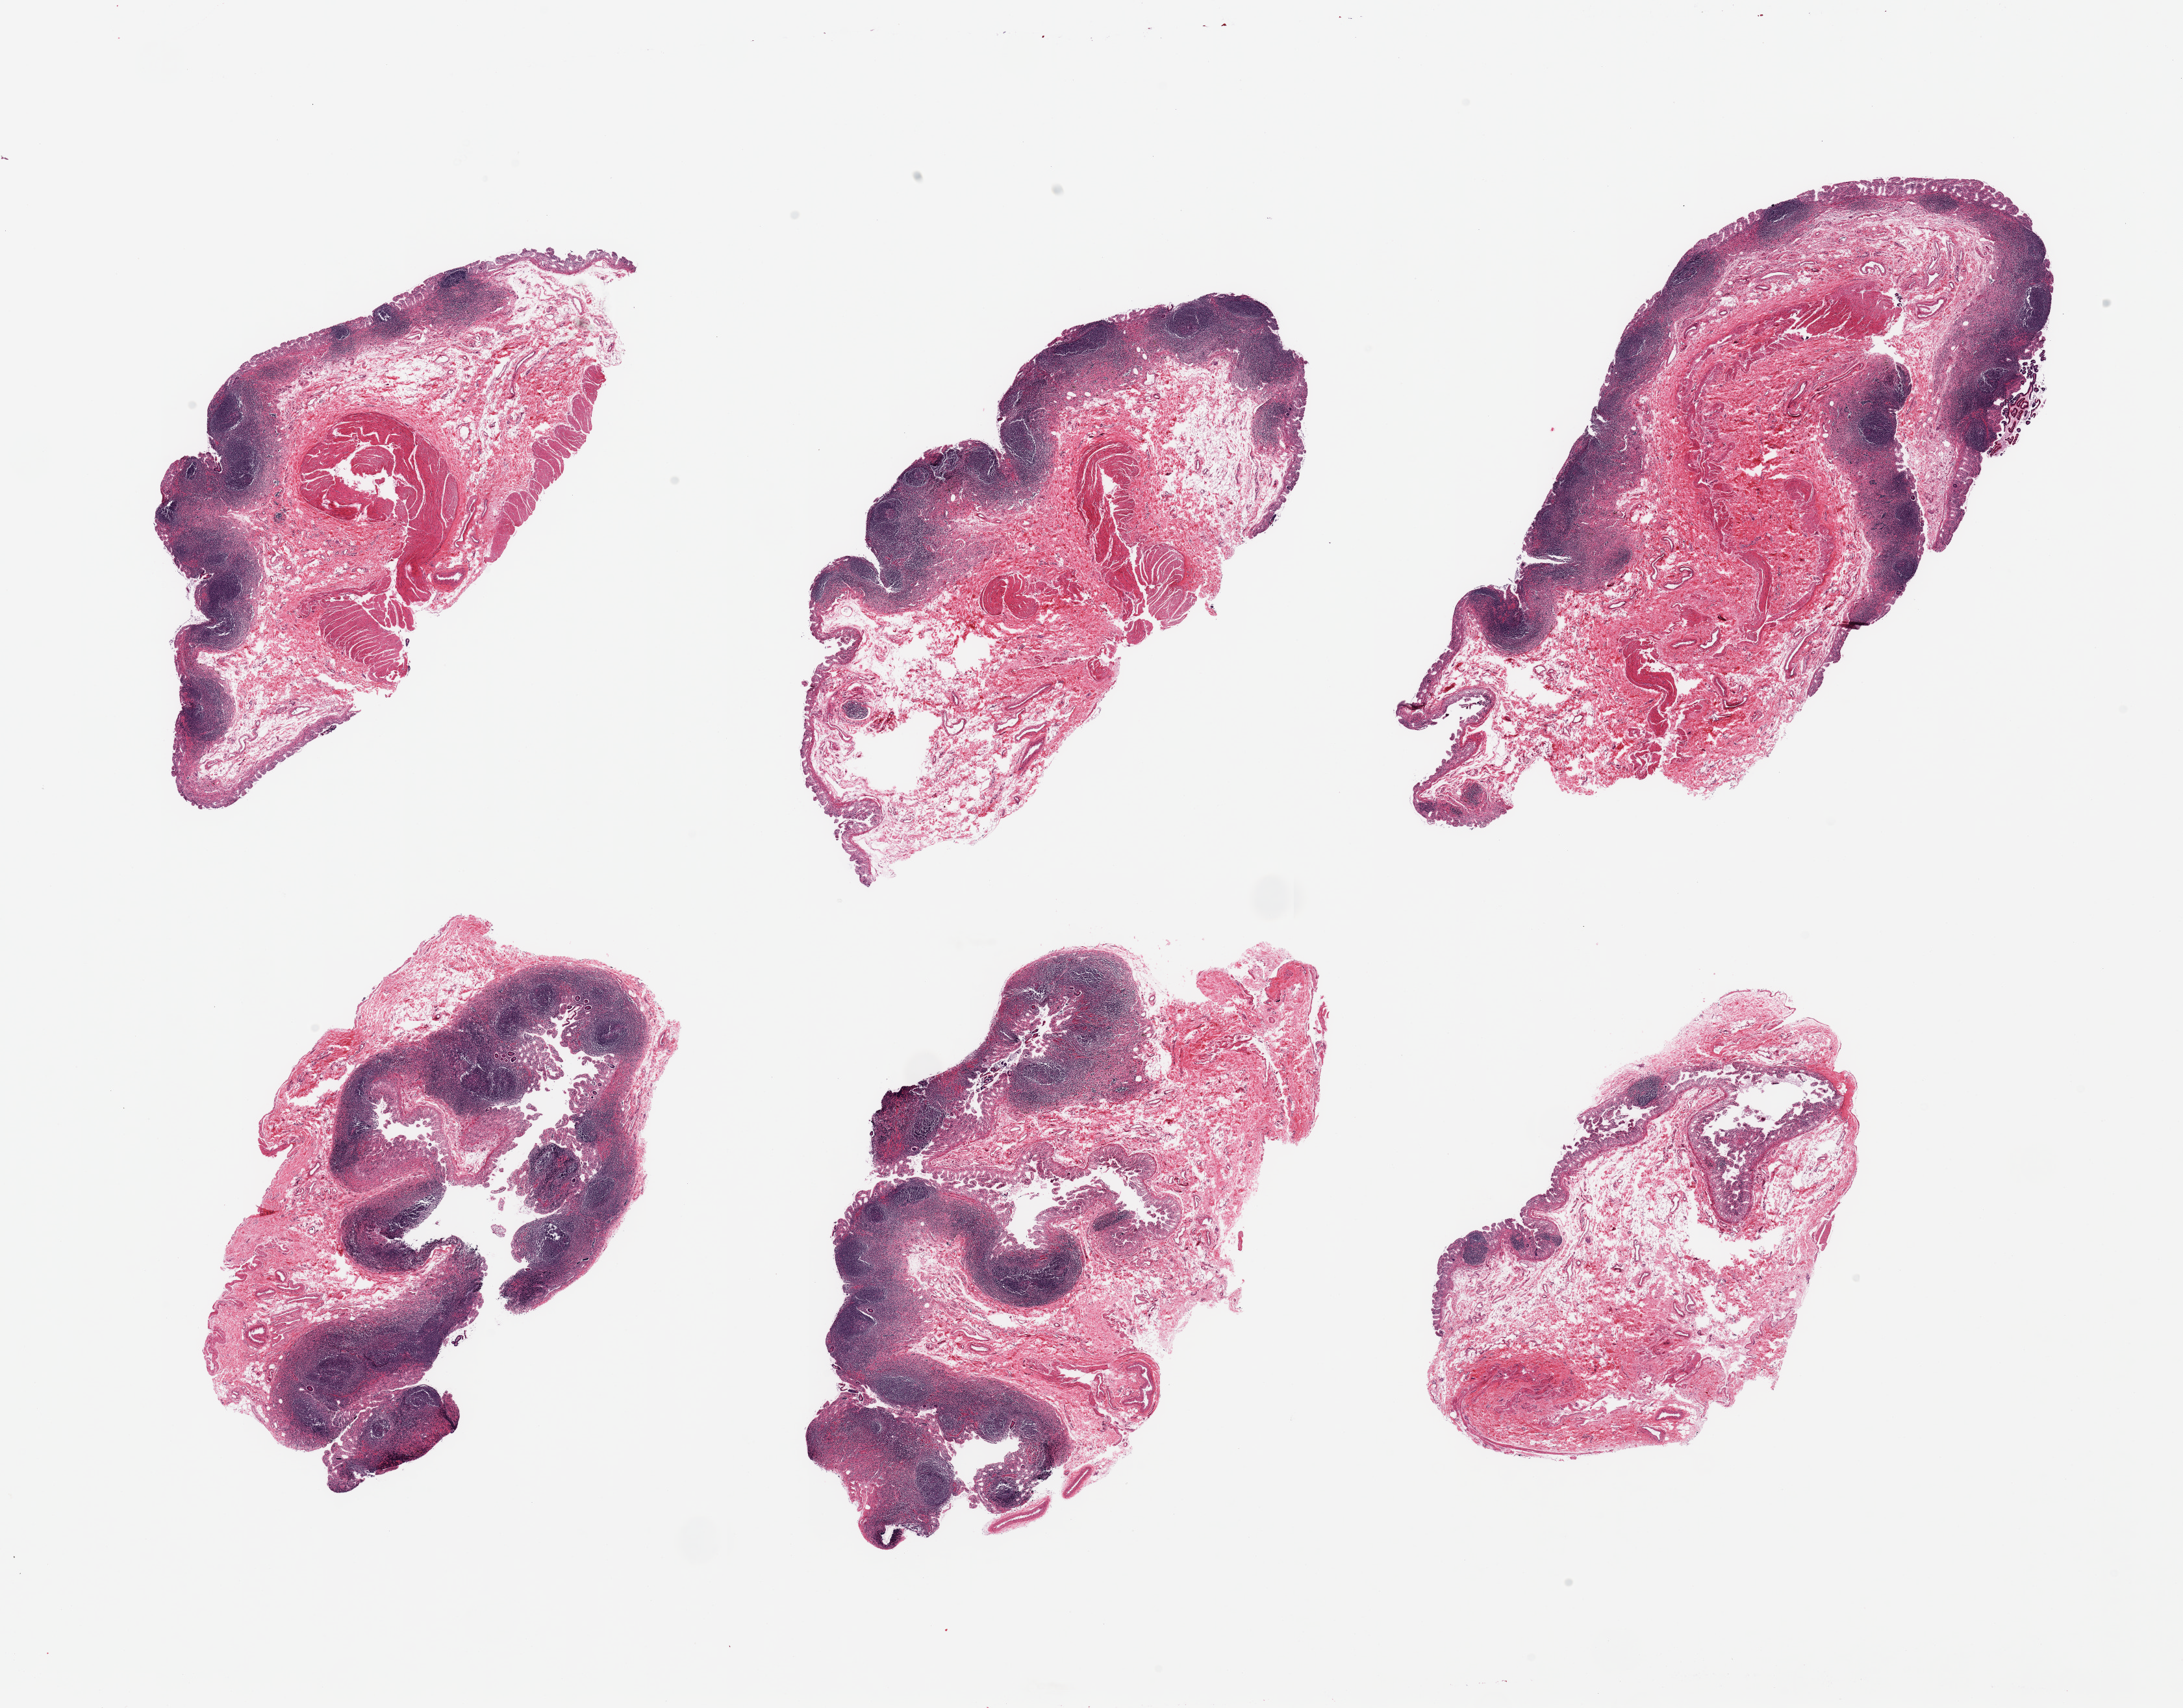
H&E whole-slide image, whole scanned area (about 26.6 x 20.8 mm, slide scanned at 20x) shown as a low-resolution overview; PAXgene-fixed, paraffin-embedded tissue; target tissue: ileum; tissue donor sample. Donor sex: male.
• review note (as recorded): 6 pieces, target lymphoid aggregates well preserved, up to ~20% tissue